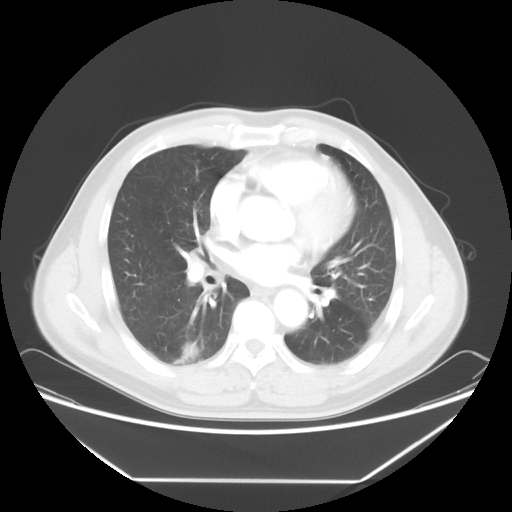
Chest CT, one axial slice. Reconstruction kernel STANDARD. 120 kVp. Lung window (W 1500 / L -600 HU). 5 mm slice thickness. 512 × 512 image matrix, field of view 418 × 418 mm. Male patient, age 50 years. Case-level facts recorded for this patient, not image findings: clinical TNM (as recorded): T1c N0 M0; histopathological grade: G3.
Annotated regions visible in this slice (bounding box drawn by a radiologist):
- lung tumour (recorded histology: adenocarcinoma): box from (x=165, y=339) to (x=207, y=373) px